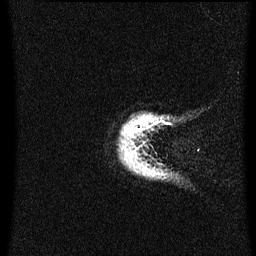
Breast MRI (dynamic contrast-enhanced), one sagittal slice; slice 59 of 60 in the series (ordered by position); dynamic contrast-enhanced series, image 2 of 3 at this slice position (ordered by acquisition); 1.5 T; TE 4.2 ms, TR 8.4 ms; 2.3 mm slice thickness; 256 × 256 image matrix, field of view 200 × 200 mm. Patient: female, 38 years. From the clinical record (not read from this slice): setting: breast cancer imaged before/during neoadjuvant chemotherapy; receptor status: HER2-positive.
Structures marked on this image (semi-automatic segmentation, software-assisted and operator-edited):
- analysis volume of interest (the breast-tissue region the enhancement analysis was run in; not a lesion): bounding box [x1, y1, x2, y2] px = [121, 114, 168, 179]
- tumour enhancement mask (voxels above the 70 % enhancement threshold inside the analysis volume of interest): [126, 128, 130, 135]